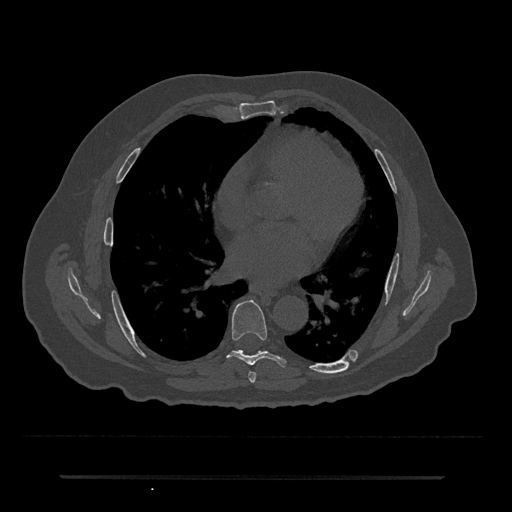
CT including the spine, one axial slice; position 383 of 797 along the scan axis; reconstruction kernel Br40s/3; 120 kVp; bone window (W 1800 / L 400 HU); 0.5 mm slice thickness; 512 × 512 image matrix, field of view 437 × 437 mm. Male patient, age 69 years. From the clinical record (not read from this slice): primary cancer: prostate.
Structures marked on this image (semi-automatic segmentation, software-assisted and operator-edited):
- T6 vertebra: bounding box <248,372,256,383> (left, top, right, bottom; pixels)
- T7 vertebra: <227,300,287,367>